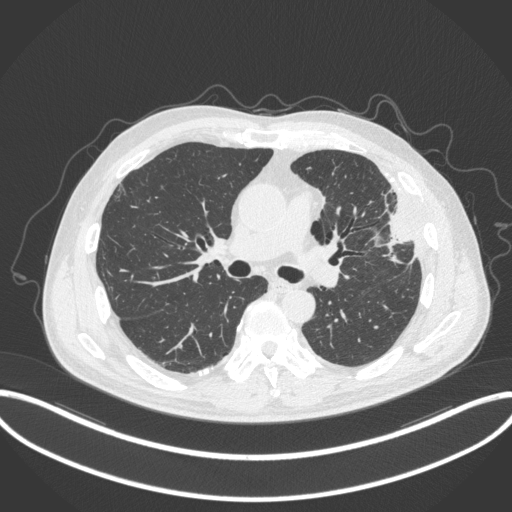
Chest CT, one axial slice. Slice 199 of 382 in the series (ordered by position). 120 kVp. Lung window (W 1500 / L -600 HU). 1 mm slice thickness. 512 × 512 image matrix. Male patient, age 64 years. Case-level facts recorded for this patient, not image findings: clinical TNM (as recorded): T4 N1 M0; histopathological grade: G3.
Structures marked on this image (rectangle marked by the reading radiologist):
- lung tumour (recorded histology: adenocarcinoma): bounding box <377,191,415,261> (left, top, right, bottom; pixels)